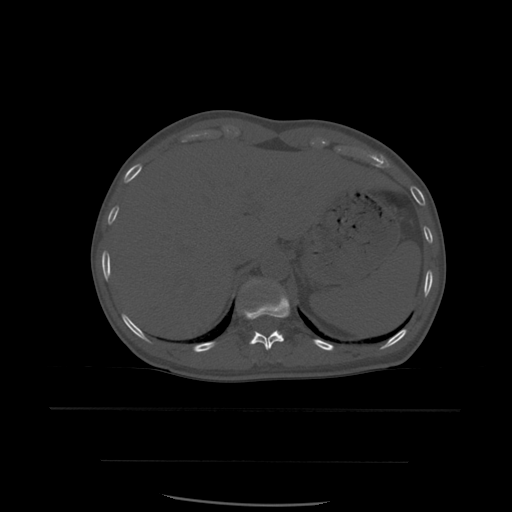
CT including the spine, one axial slice; position 291 of 574 along the scan axis; bone window (W 1800 / L 400 HU); 1.25 mm slice thickness; 512 × 512 image matrix, field of view 392 × 392 mm. Patient age 48 years. From the clinical record (not read from this slice): primary cancer: lung.
Outlined on this slice (semi-automatically segmented with operator editing):
- T11 vertebra: box from (x=240, y=291) to (x=290, y=350) px
- T12 vertebra: (x=247, y=280)–(x=262, y=287)